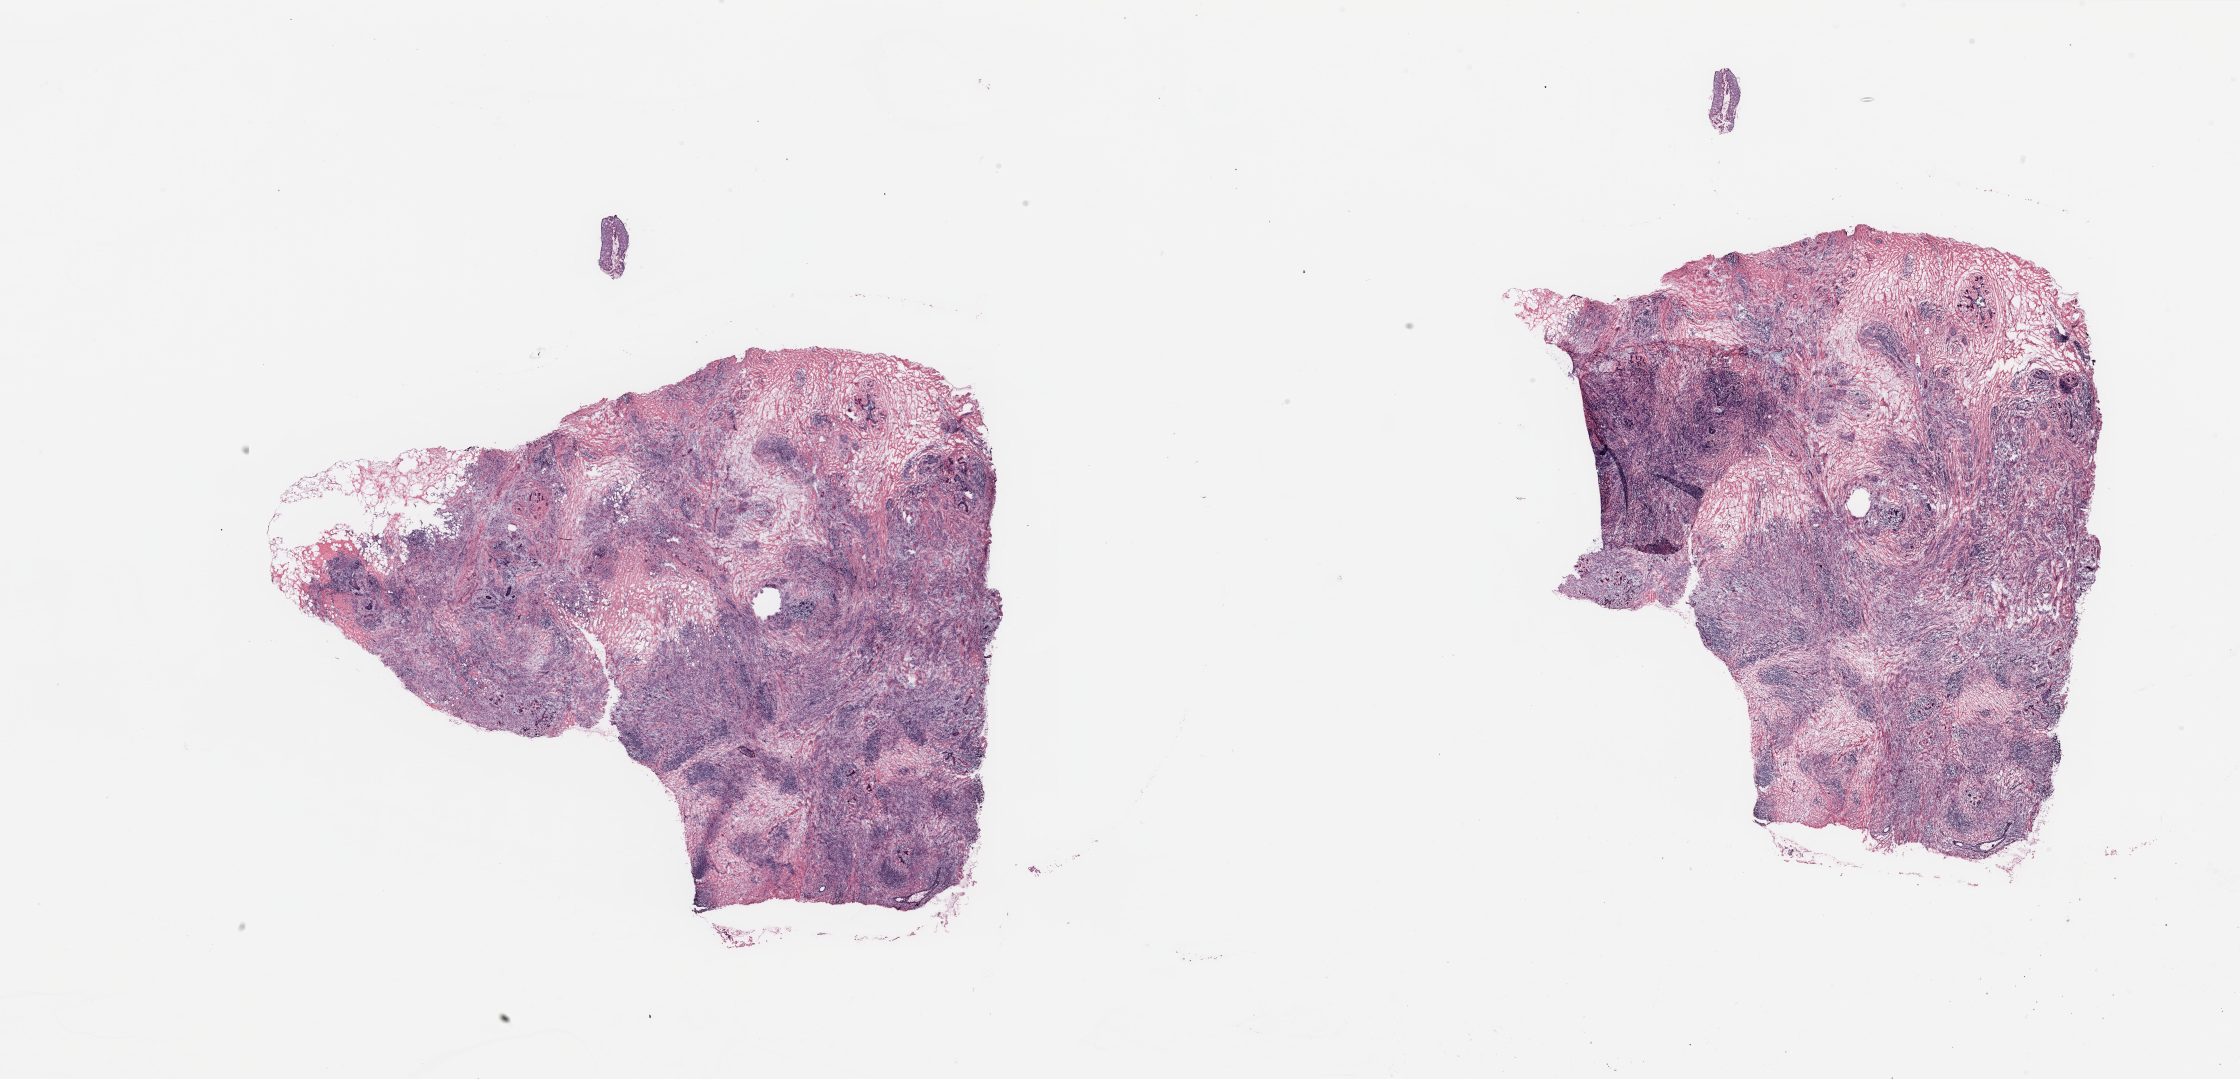
Digitized H&E tissue section (whole slide), low-resolution overview of the scanned area, about 35.4 x 17.1 mm (acquisition: 20x scan); breast, tissue type not recorded.
Patient diagnosis (cohort enrolment): breast cancer (breast).